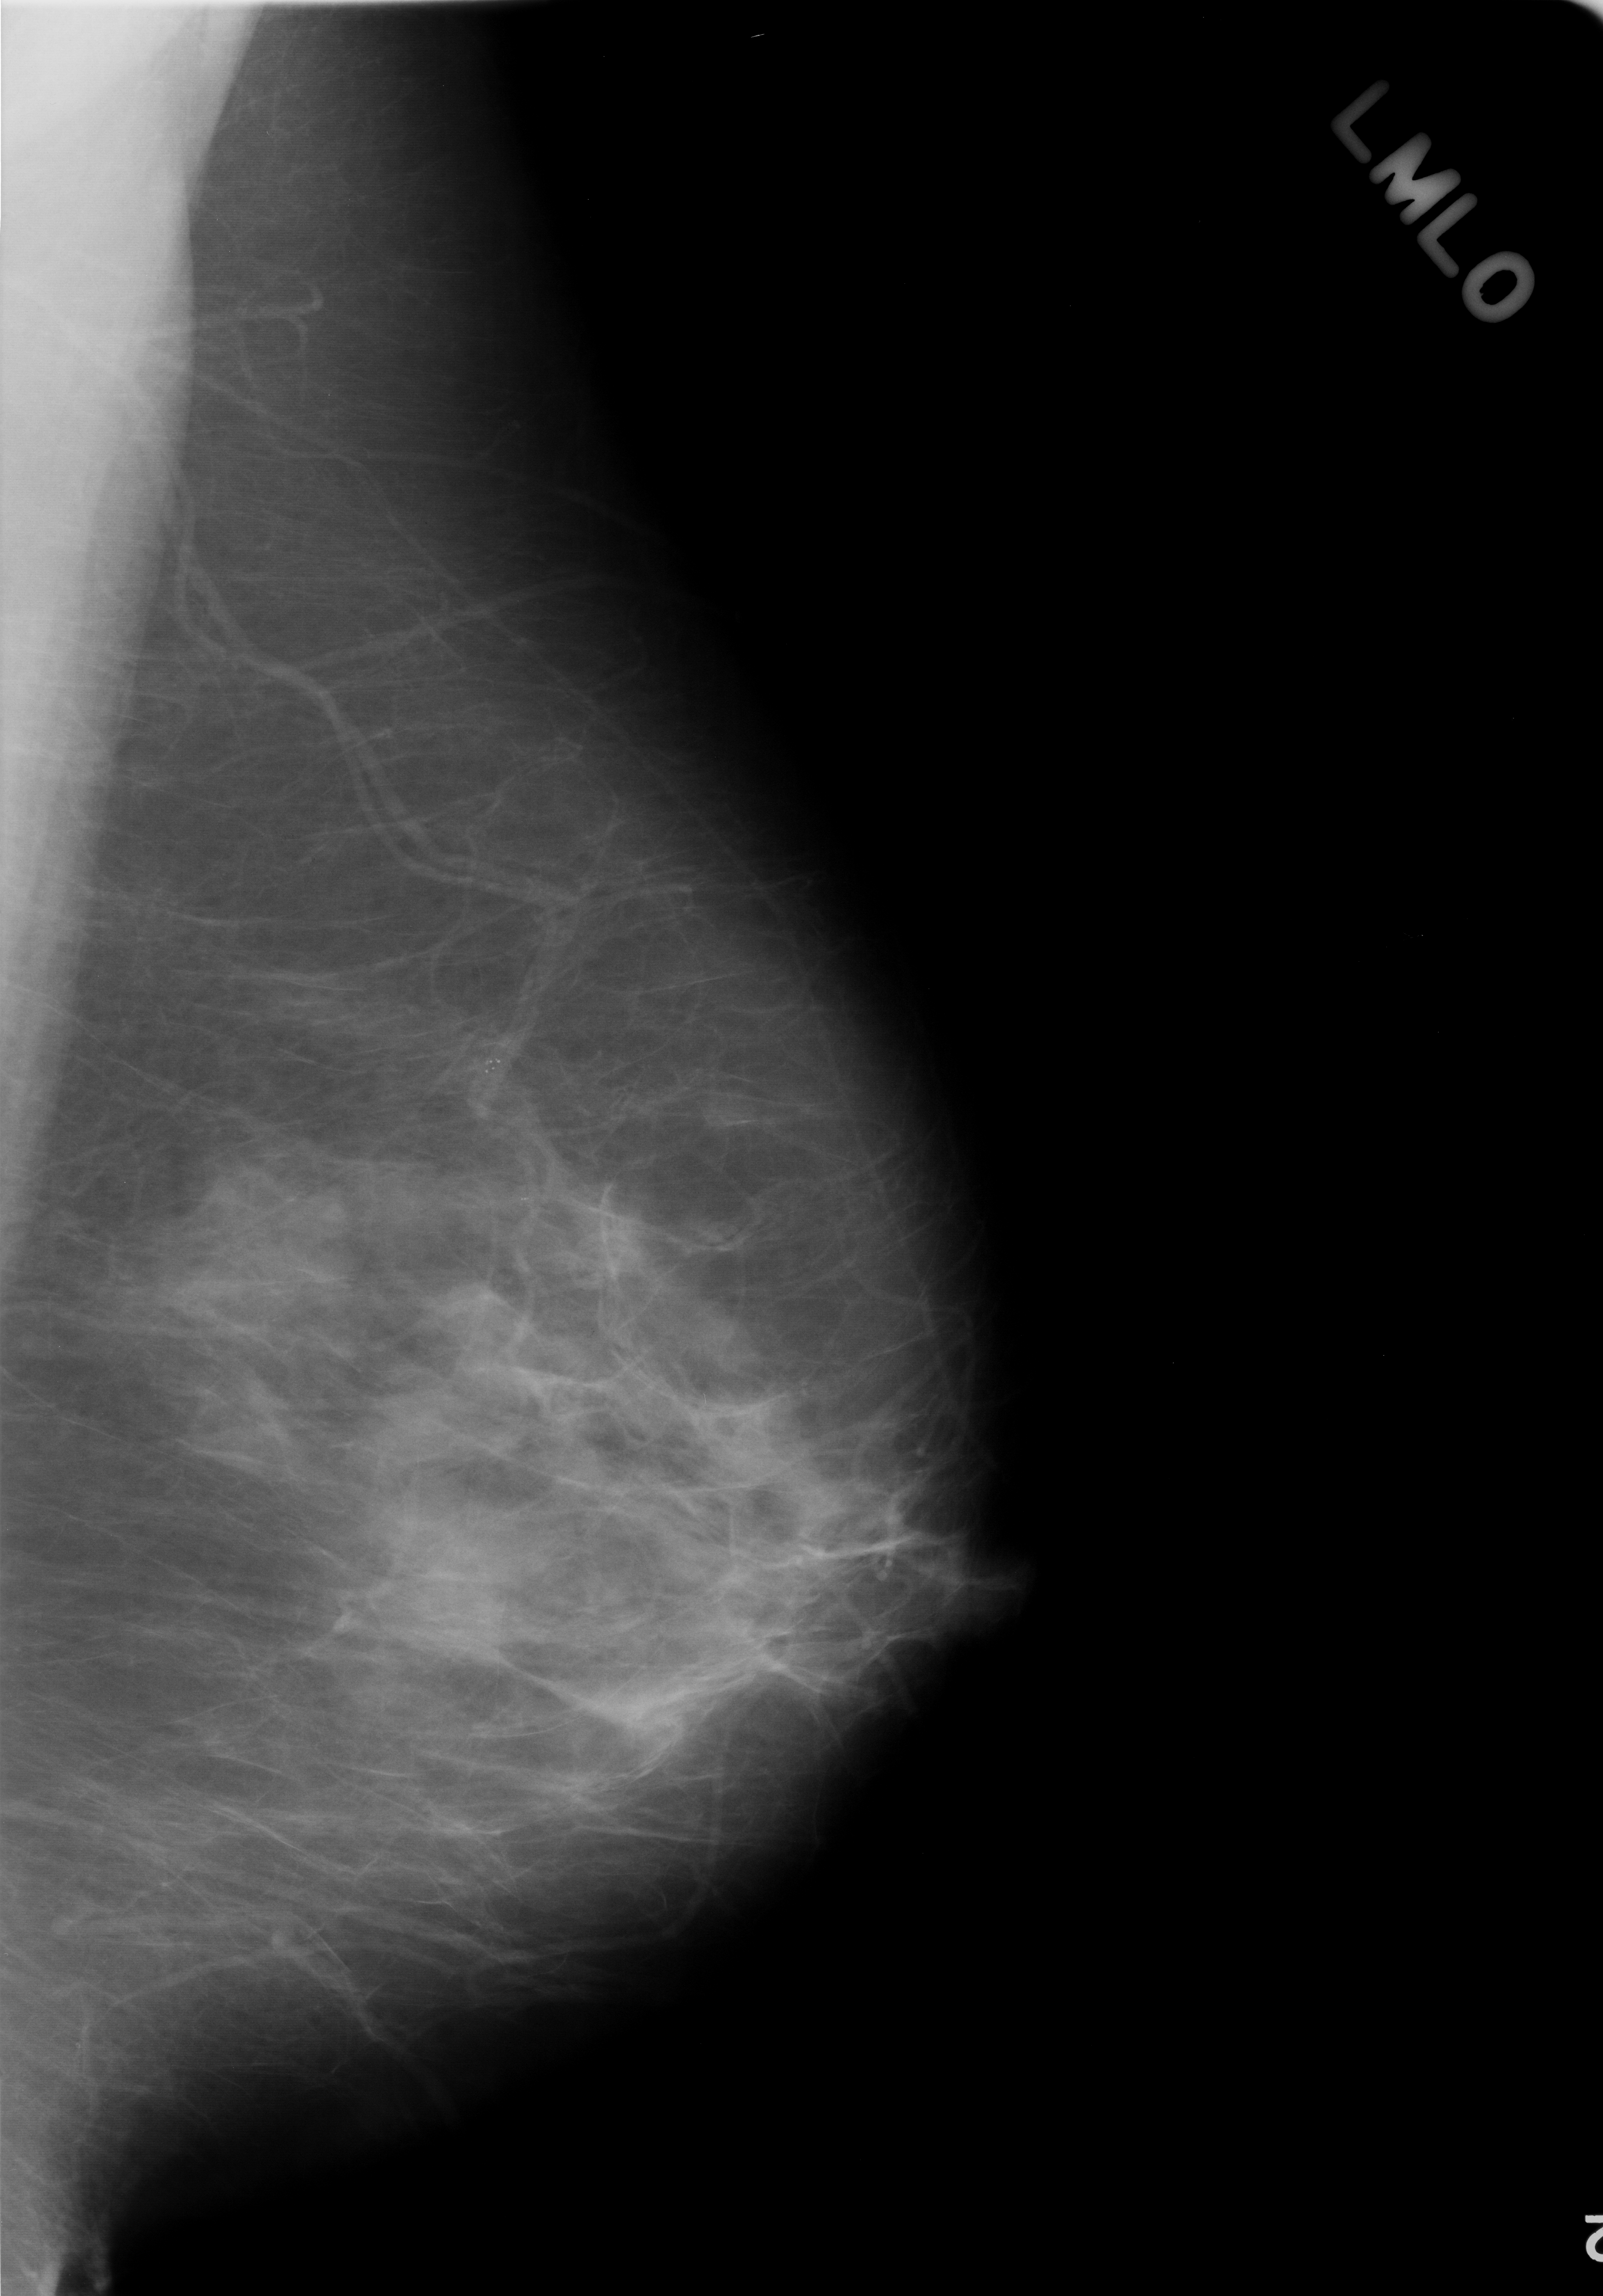
Mammogram (digitized film). Left breast. MLO view. 1603 × 2296 image matrix.
Marked abnormalities (boxes around the expert regions of interest):
- calcifications, morphology punctate, distribution clustered; BI-RADS assessment category 3; pathology result (as recorded, not read from the image): benign: bounding box (x1, y1, x2, y2) in pixels: (419, 990, 568, 1133)